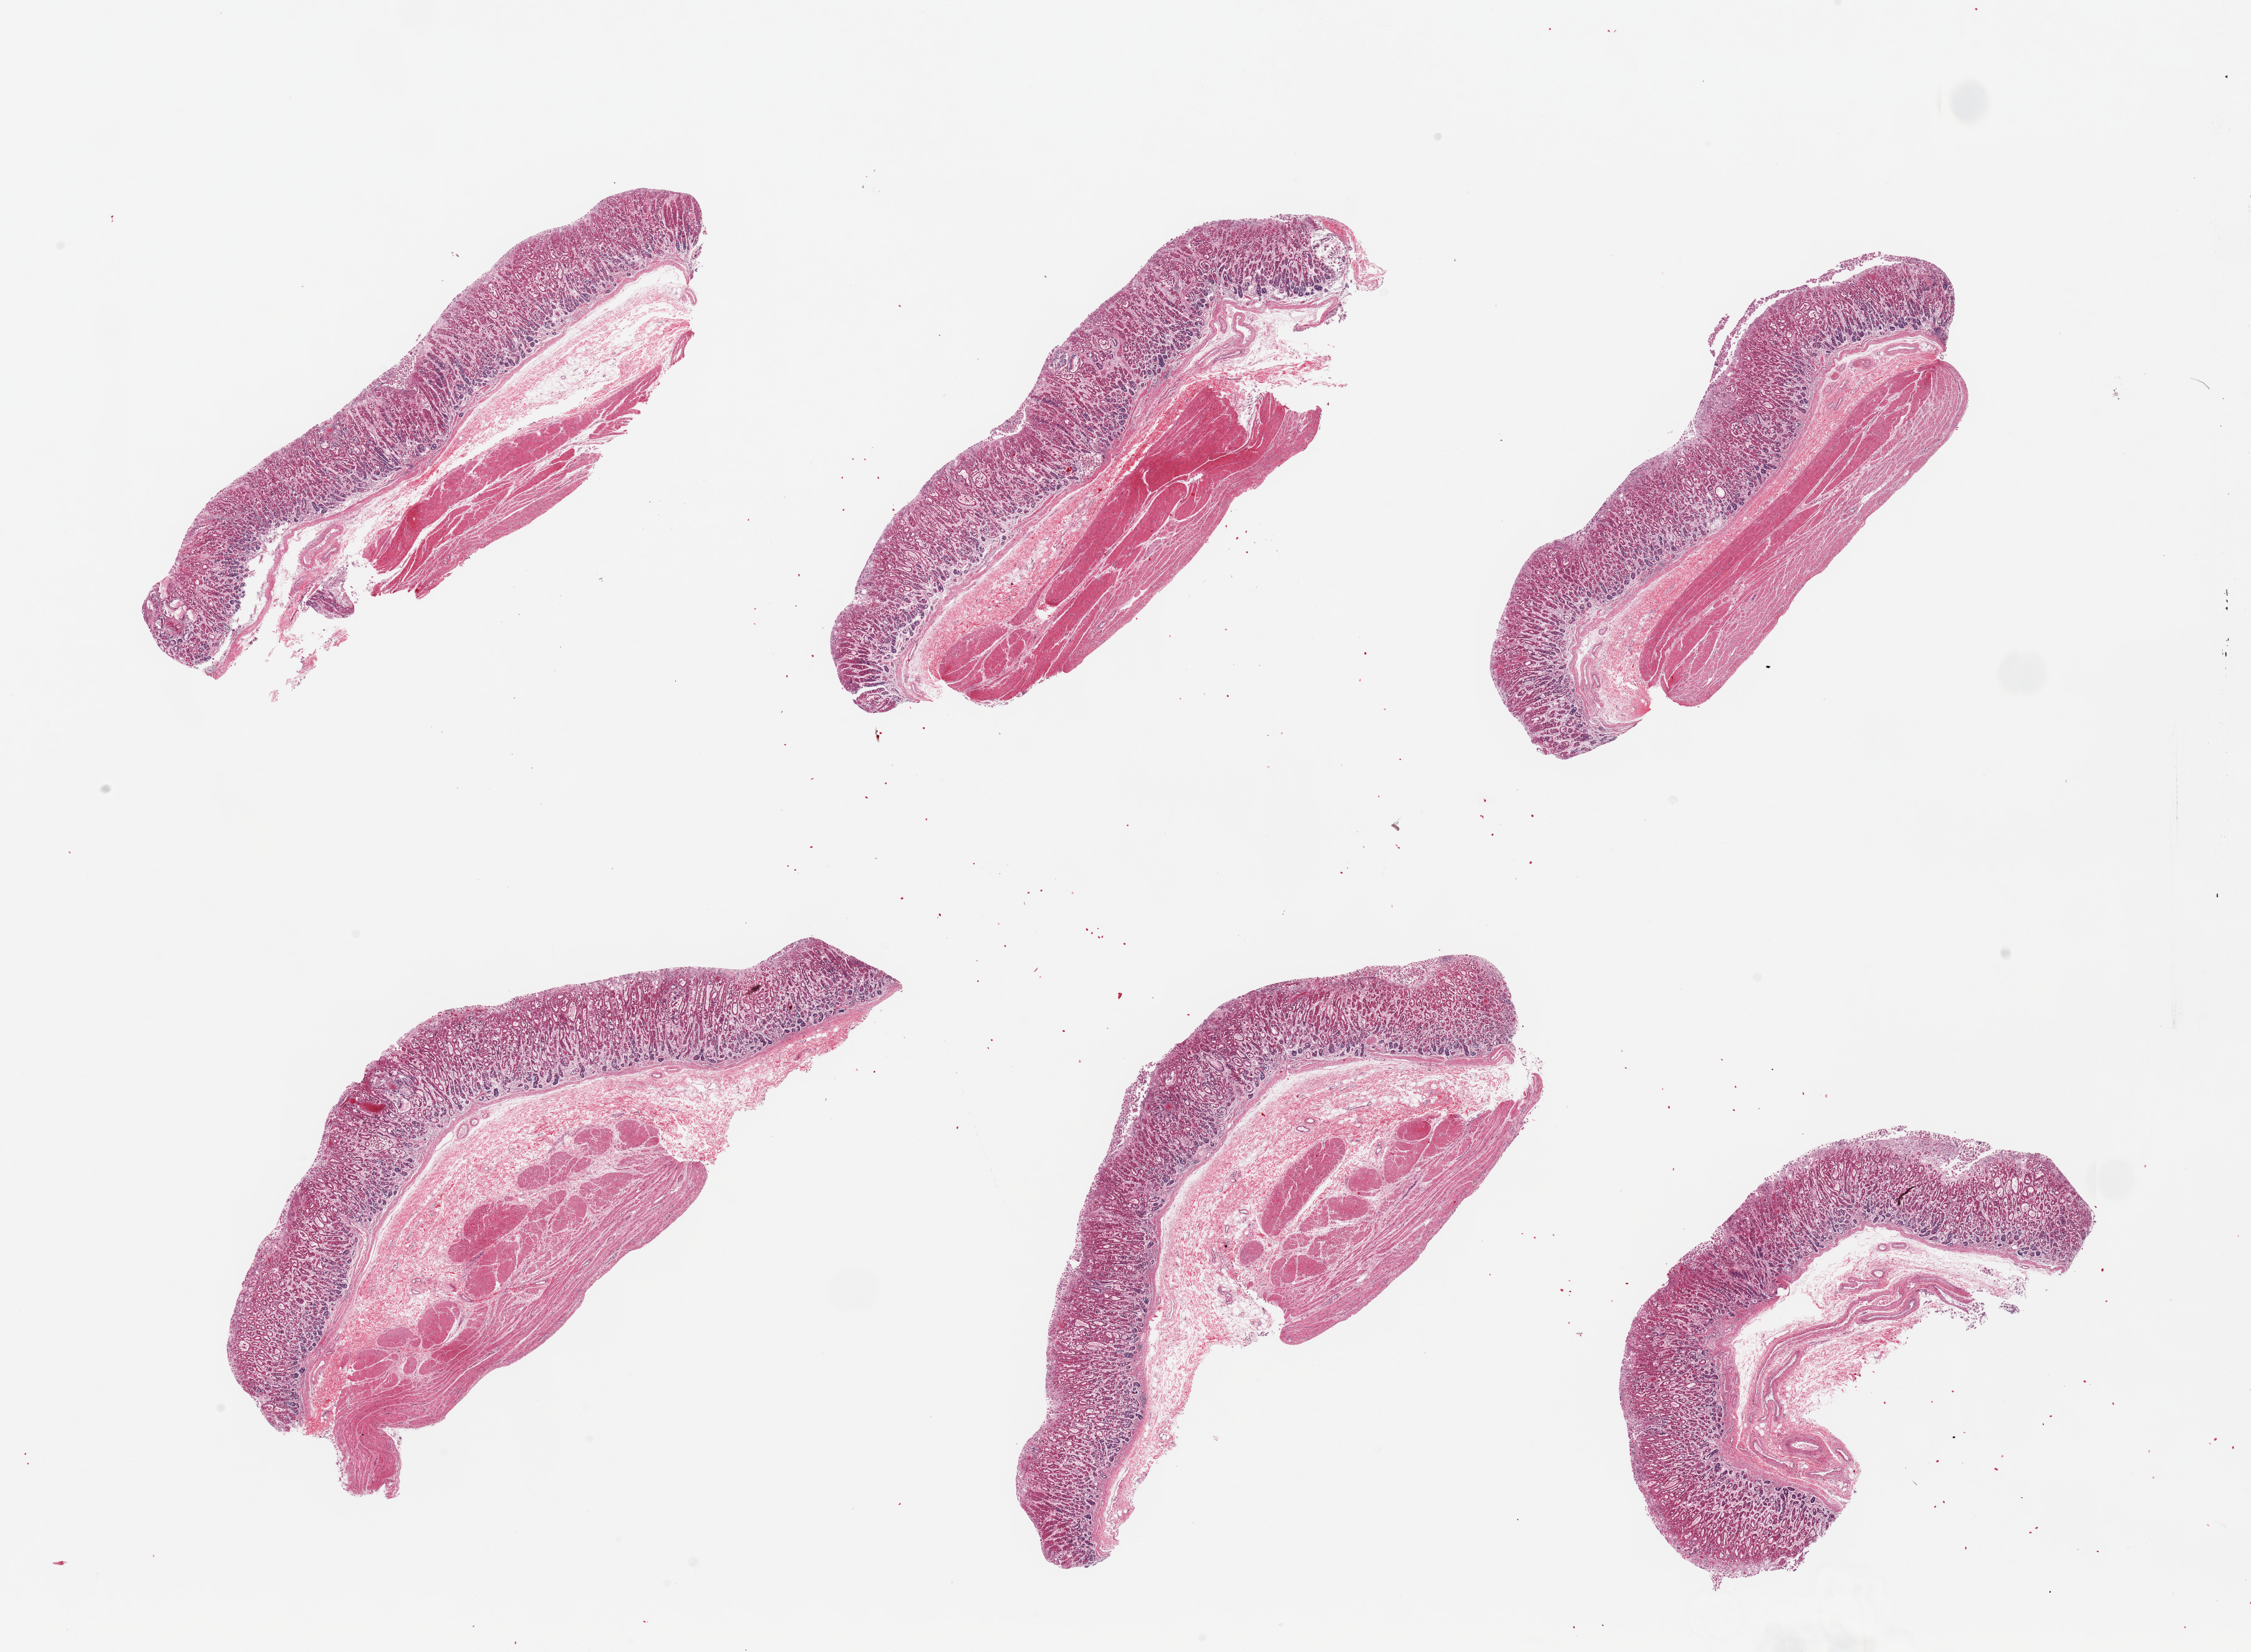
Whole-slide image, hematoxylin and eosin (H&E) stain — shown as a low-resolution overview of the whole scanned area (about 28.5 x 20.9 mm, slide scanned at 20x). PAXgene-fixed, paraffin-embedded tissue. Sampled site (target tissue): stomach. Tissue donor sample. Donor: male.
Review note (as recorded): 6 pieces; 5 have full thickness of wall; 1 lacks muscularis.